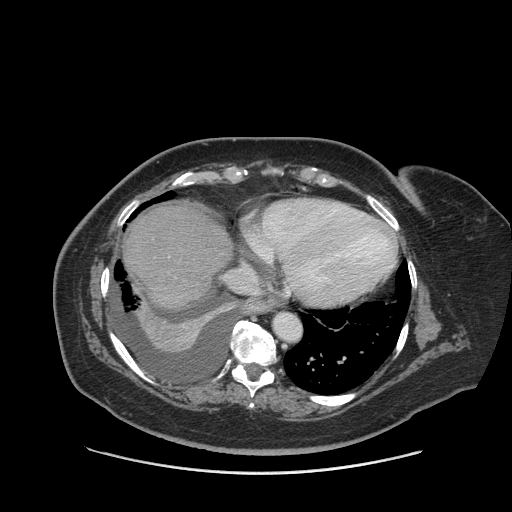
Contrast-enhanced abdominal CT (liver protocol), one axial slice. Position 77 of 91 along the scan axis. Soft-tissue window (W 400 / L 40 HU). 2.5 mm slice thickness. 512 × 512 image matrix, field of view 420 × 420 mm. Case-level facts recorded for this patient, not image findings: diagnosis: hepatocellular carcinoma (patient treated with transarterial chemoembolisation; whether this scan precedes or follows treatment is not stated here); TNM stage (as recorded): Stage-I.
Outlined on this slice (semi-automatic segmentation, software-assisted and operator-edited):
- abdominal aorta: box from (x=273, y=313) to (x=301, y=341) px
- liver parenchyma outside the tumour (the mass and vessels are separate outlines, so this box may not span the whole liver): (x=124, y=204)–(x=232, y=308)